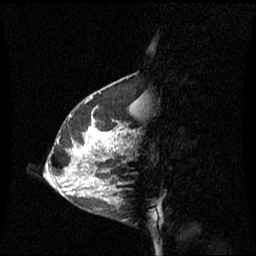
Breast MRI (dynamic contrast-enhanced), one sagittal slice. Slice 22 of 60 in the series (ordered by position). Dynamic contrast-enhanced series, image 2 of 3 at this slice position (ordered by acquisition). 1.5 T. TE 4.2 ms, TR 8.4 ms. 256 × 256 image matrix. Female patient, age 42 years. Case-level facts recorded for this patient, not image findings: setting: breast cancer imaged before/during neoadjuvant chemotherapy; receptor status: HR-positive, HER2-negative.
Annotated regions visible in this slice (semi-automatically segmented with operator editing):
- analysis volume of interest (the breast-tissue region the enhancement analysis was run in; not a lesion): bounding box (x1, y1, x2, y2) in pixels: (68, 100, 137, 201)
- tumour enhancement mask (voxels above the 70 % enhancement threshold inside the analysis volume of interest): (92, 116, 101, 135)